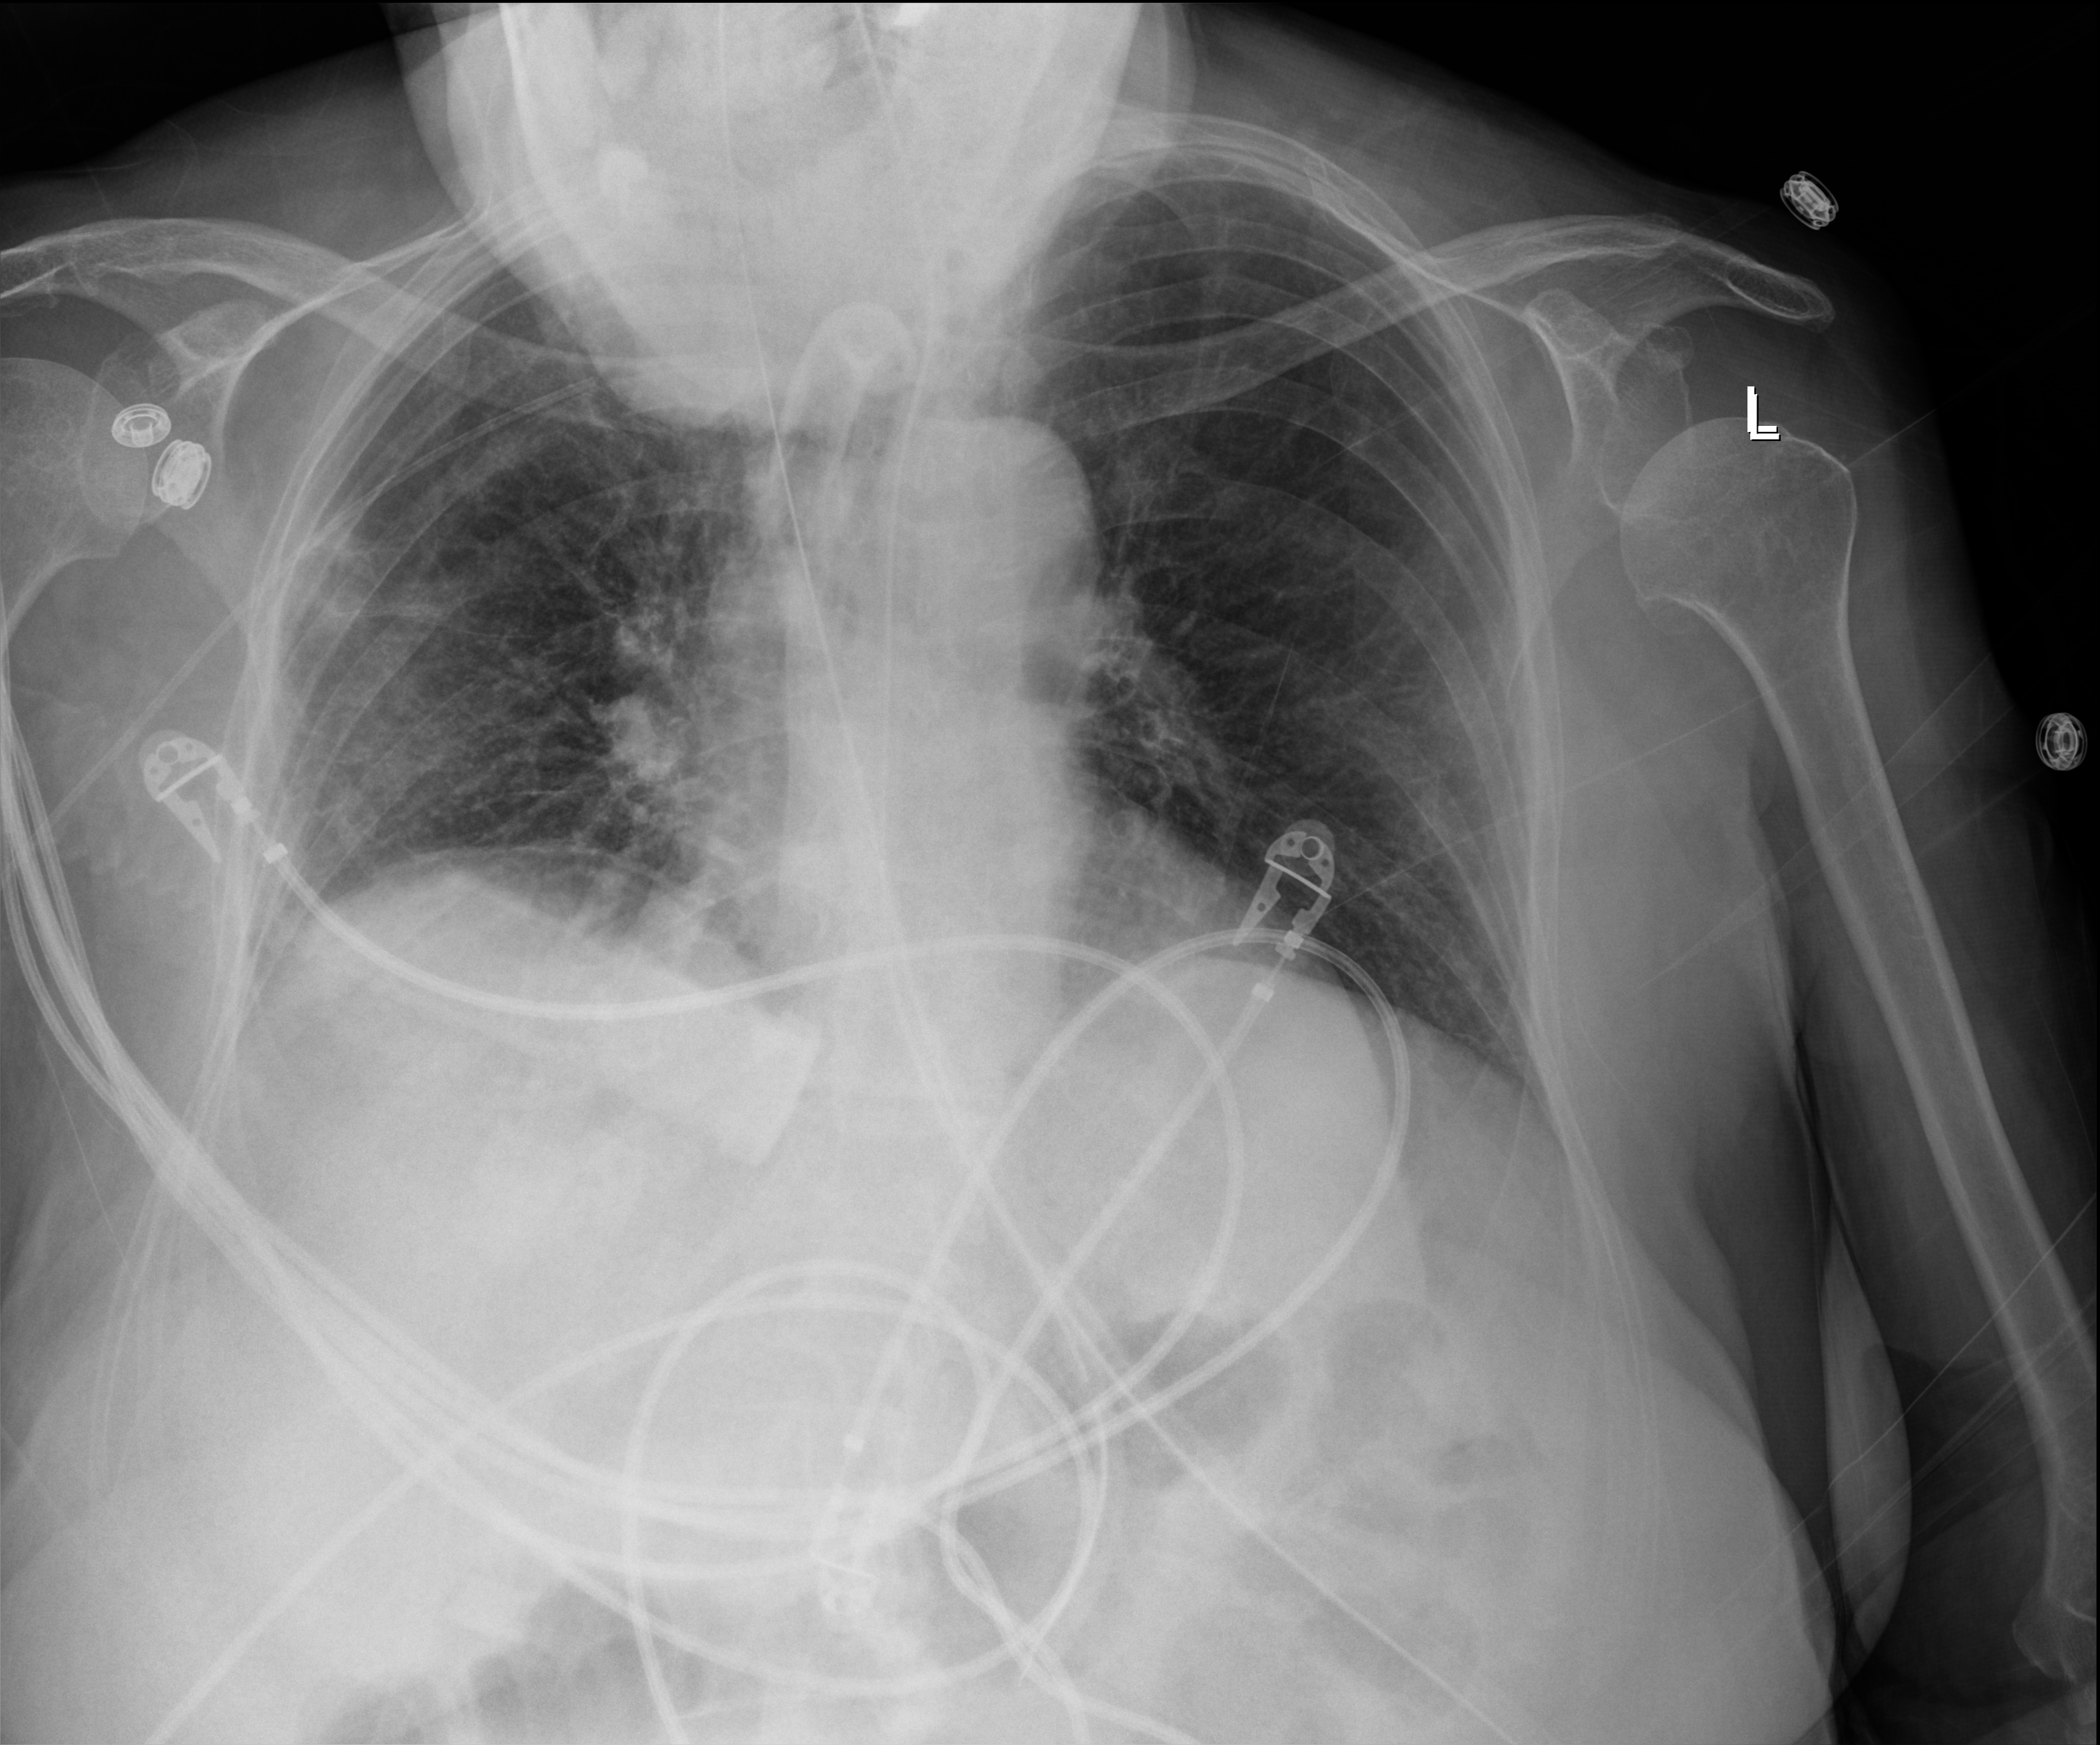
Chest radiograph, anteroposterior (AP) projection. Female patient hospitalised with COVID-19, age 75–90 years.
From the hospital-stay record, not from the radiograph (when in the stay this image was taken is not recorded): COPD (admission record): no; diabetes (admission record): no.